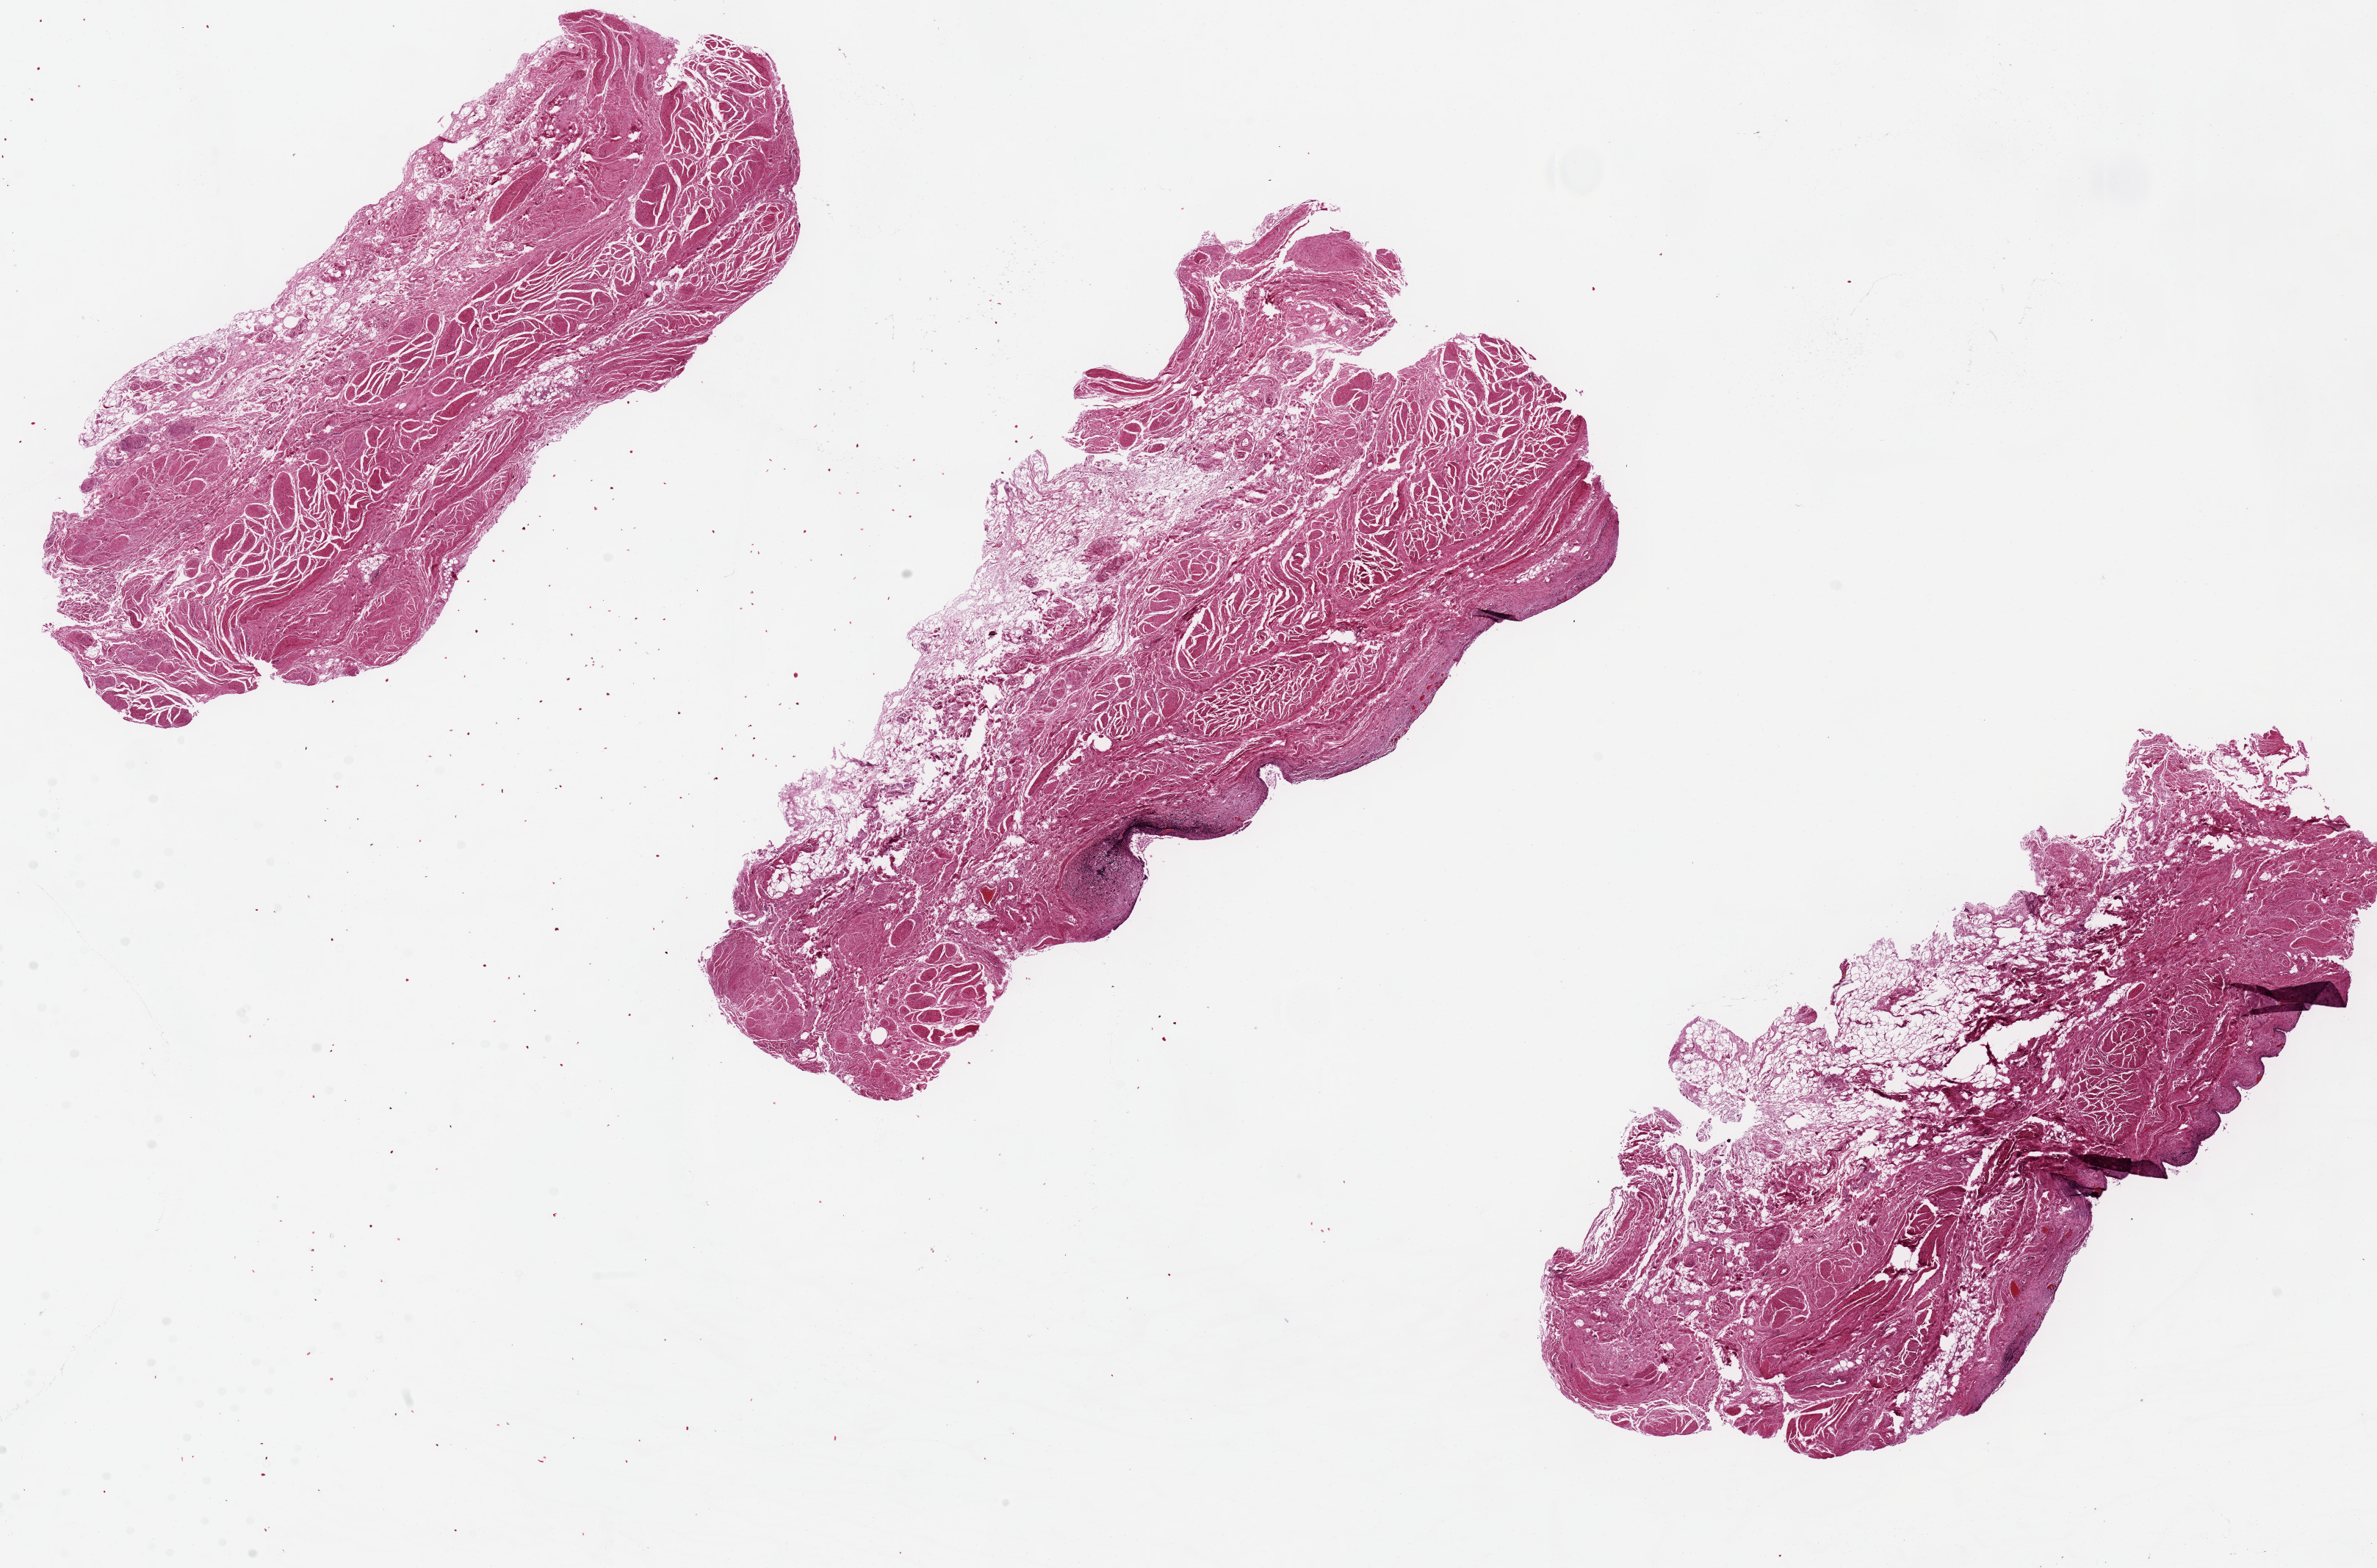
Whole-slide image, haematoxylin and eosin stain, brightfield — shown as a low-resolution overview of the whole scanned area (about 25.6 x 16.9 mm, acquisition: 20x scan); PAXgene-fixed, paraffin-embedded tissue; section of urinary bladder (target tissue); tissue donor sample. Donor sex: female.
Pathologist's review note for this sample: Urothelium 100% sloughed.